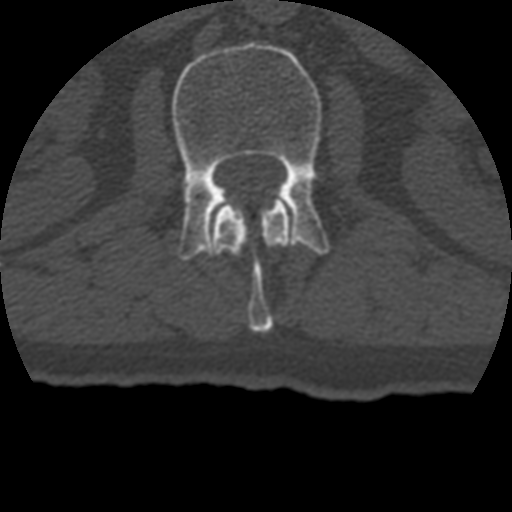
CT including the spine, one axial slice; position 127 of 399 along the scan axis; reconstruction kernel STANDARD; 120 kVp; bone window (W 1800 / L 400 HU); 512 × 512 image matrix. Patient age 69 years. Case-level facts recorded for this patient, not image findings: primary cancer: prostate.
Structures marked on this image (semi-automatically segmented with operator editing):
- L1 vertebra: bounding box (x1, y1, x2, y2) in pixels: (211, 198, 292, 332)
- L2 vertebra: (172, 42, 330, 260)